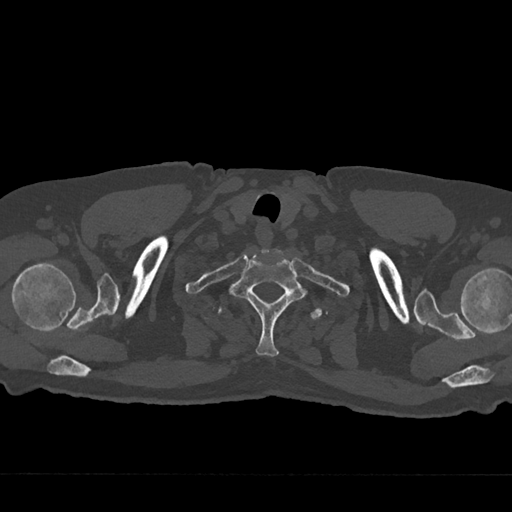
CT including the spine, one axial slice. Slice 656 of 797 in the series (ordered by position). Reconstruction kernel Br40s/3. 120 kVp. Bone window (W 1800 / L 400 HU). 512 × 512 image matrix, field of view 377 × 377 mm. Male patient, age 75 years. Case-level facts recorded for this patient, not image findings: primary cancer: renal; vertebrae with lytic lesions (as recorded): T4.
Outlined on this slice (semi-automatically segmented with operator editing):
- T1 vertebra: bounding box [x1, y1, x2, y2] px = [228, 249, 308, 357]
- T2 vertebra: [218, 292, 322, 320]